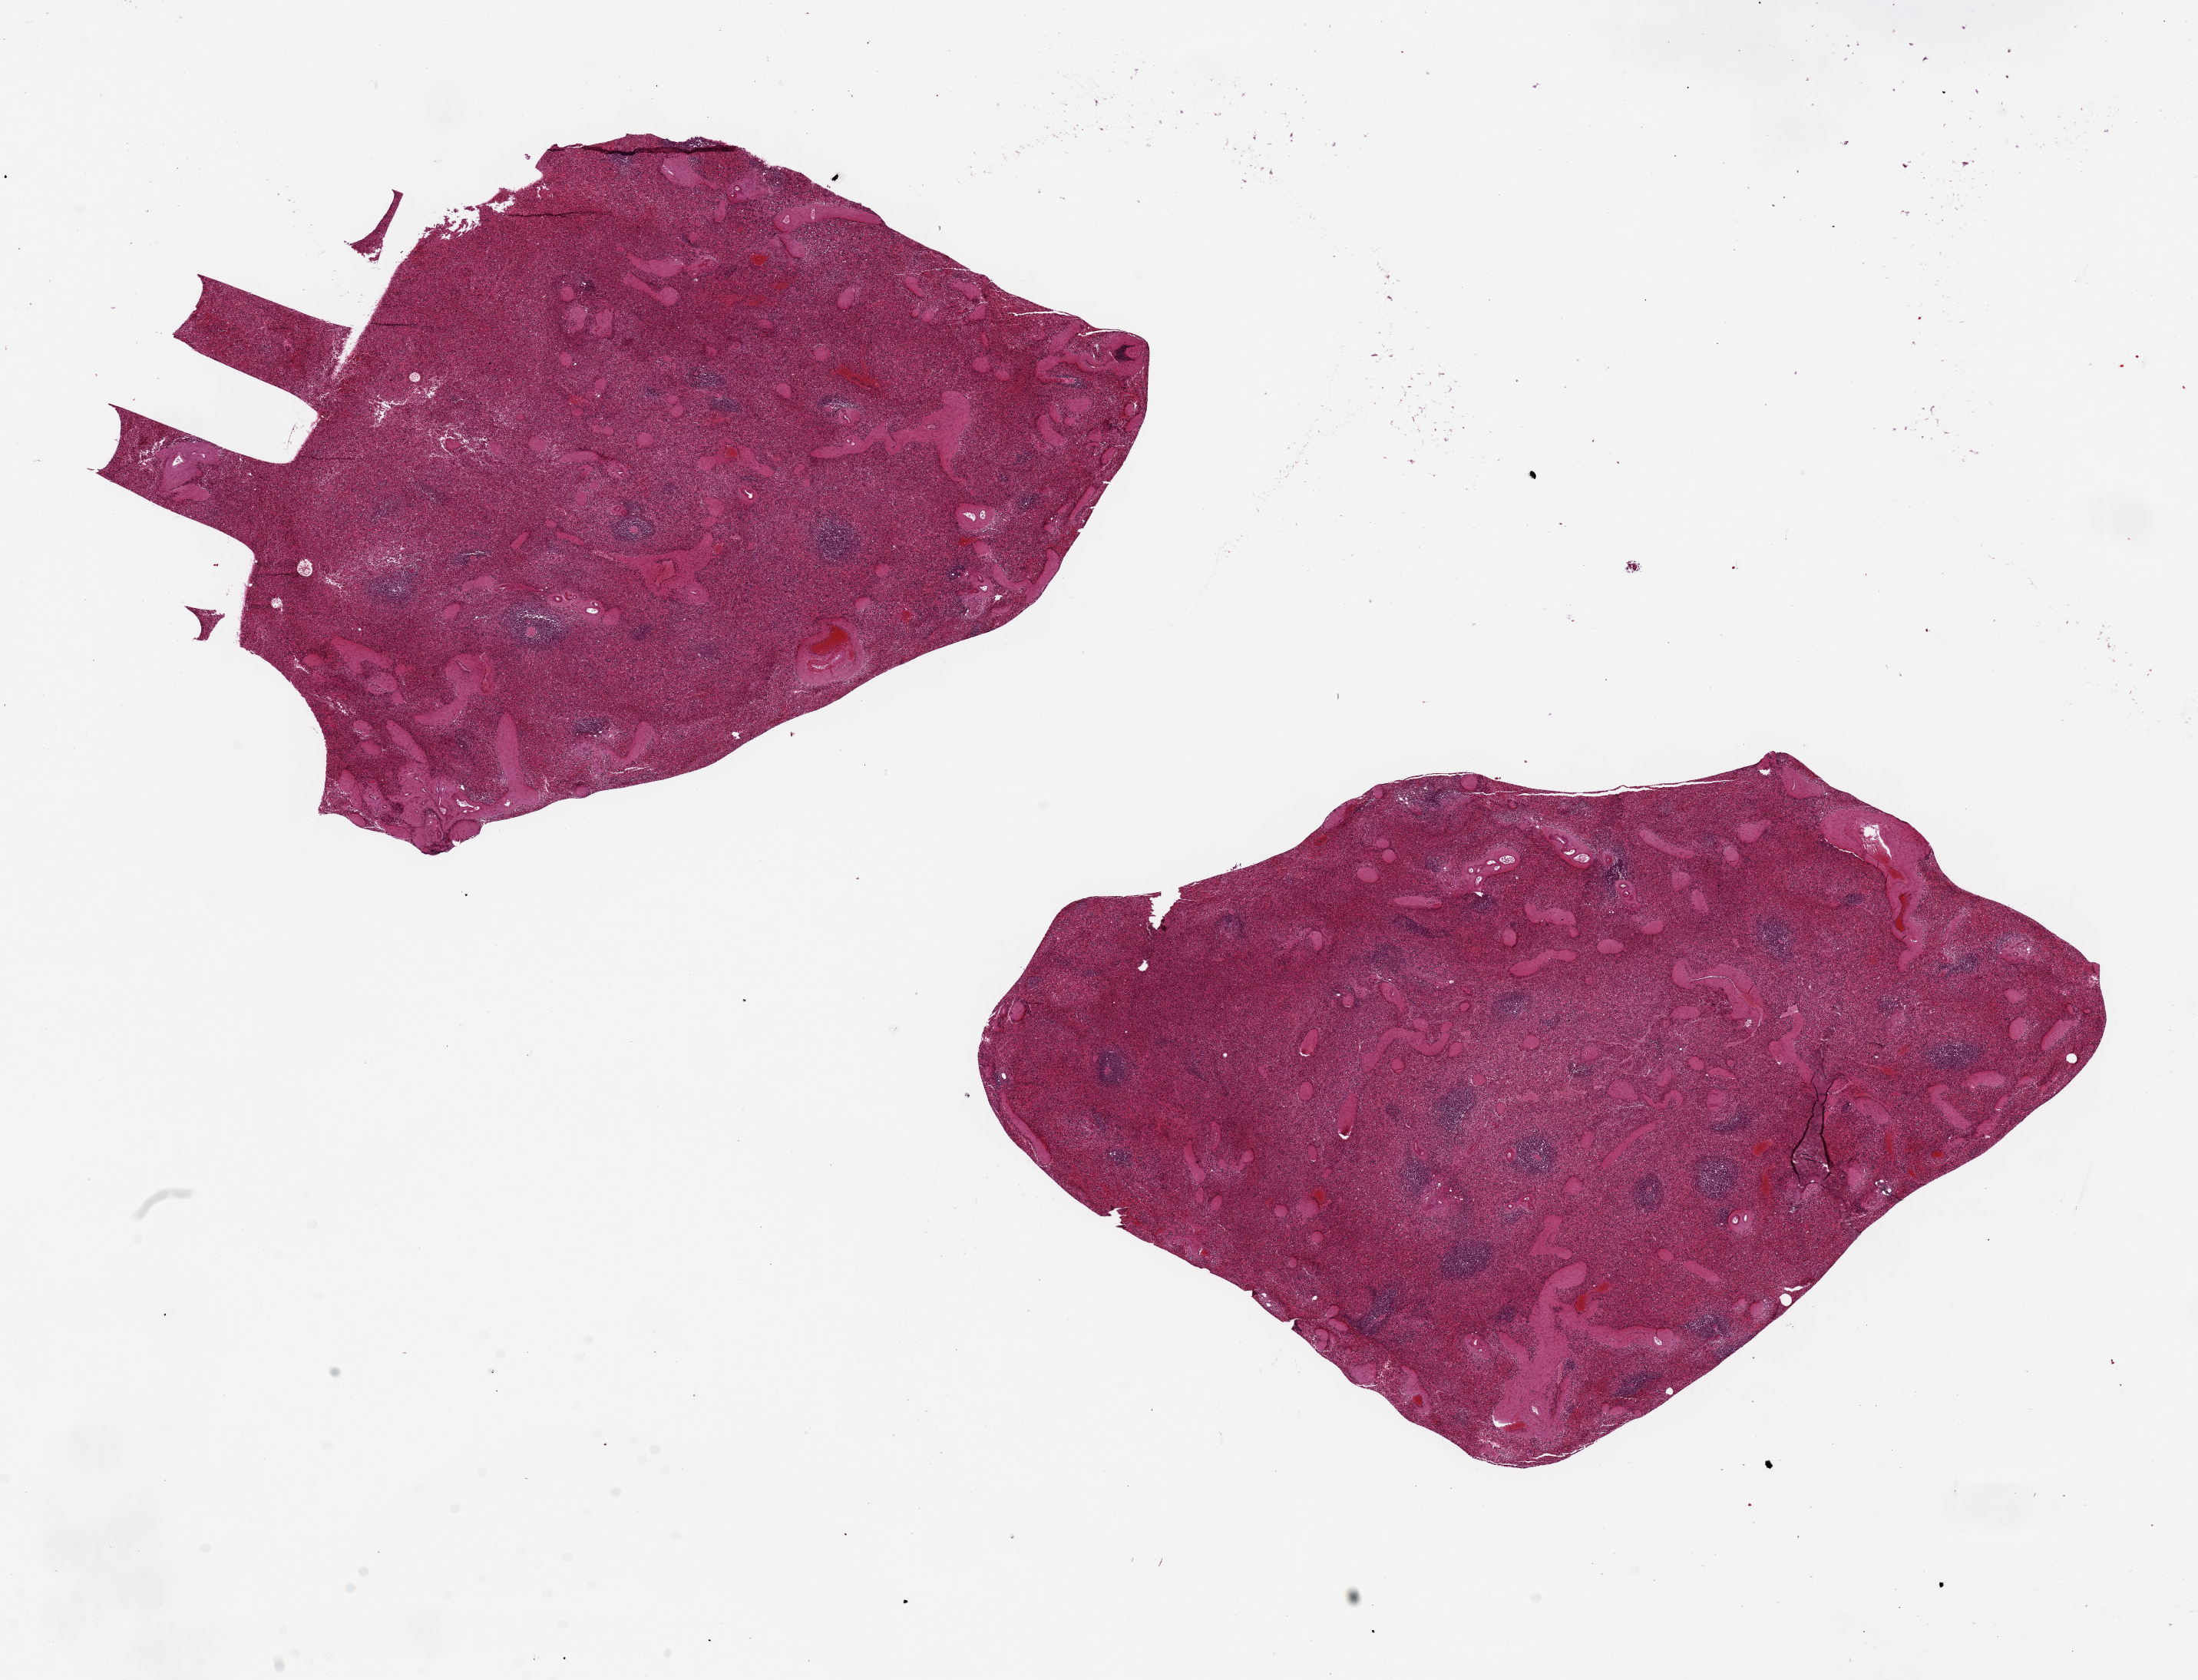
Whole-slide image, H&E stain — shown as a low-resolution overview of the whole scanned area (about 22.6 x 17.3 mm). PAXgene-fixed paraffin-embedded (PFPE) section. Target tissue: spleen. Tissue donor sample. Male donor.
Review note (as recorded): 2 pieces, 10x9 & 8x8mm; moderate congestion.